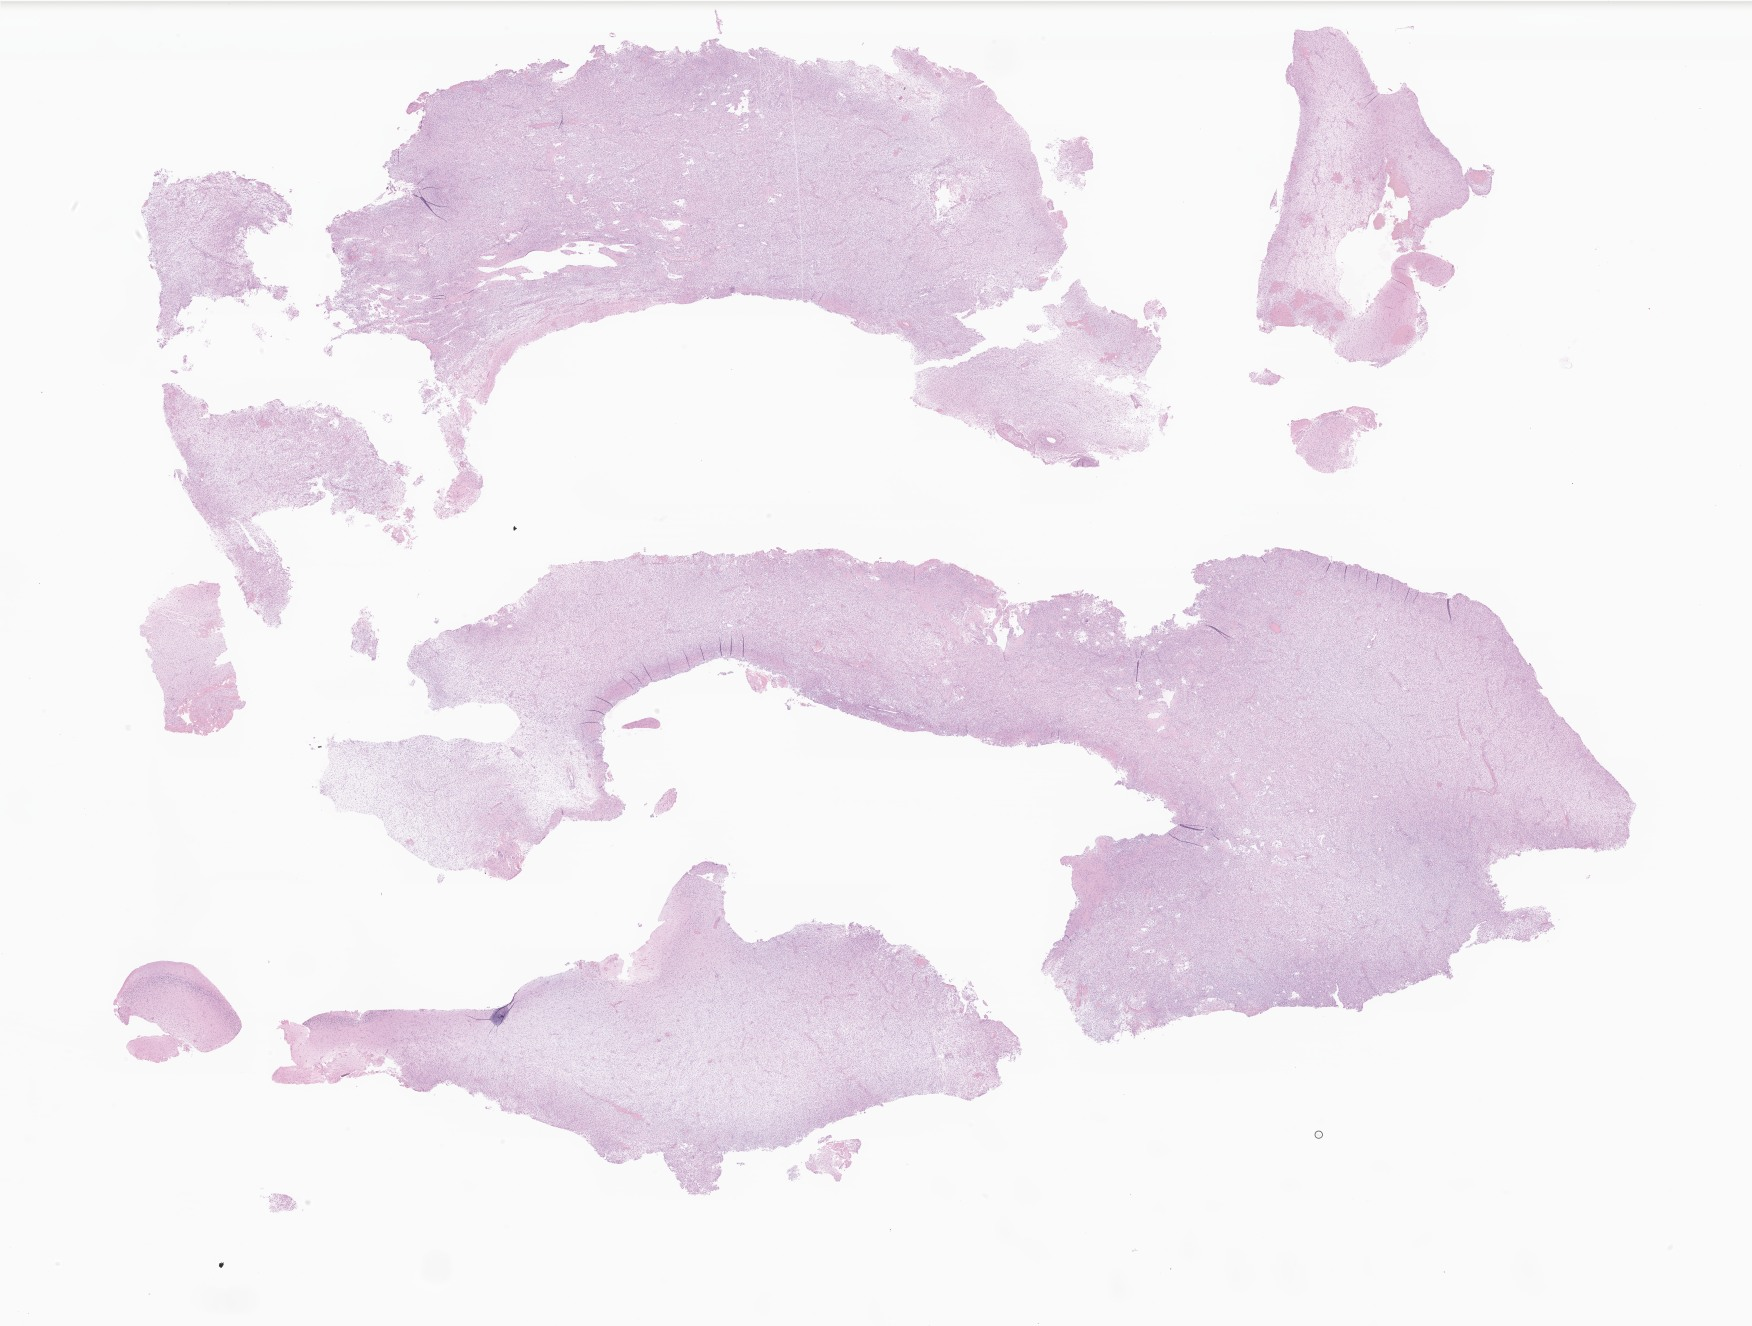
Whole-slide image, hematoxylin and eosin (H&E) stain of tumor tissue from the cerebellum — a low-resolution overview of the entire scanned area, about 29.6 x 22.4 mm; FFPE section. Patient: female, age 38 months.
• diagnosis: Pilocytic astrocytoma